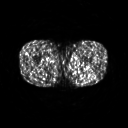
FDG PET of an extremity soft-tissue mass (from a PET/CT study), one axial slice. Position 231 of 267 along the scan axis. 128 × 128 image matrix, field of view 500 × 500 mm. Male patient, age 27 years. Case-level facts recorded for this patient, not image findings: histological type: extraskeletal osteosarcoma; grade: high; site of the primary tumour: left adductur.
Structures marked on this image (expert contour drawn on MRI and transferred to this co-registered scan by the dataset authors):
- gross tumour volume (mass): bounding box <67,60,93,78> (left, top, right, bottom; pixels)